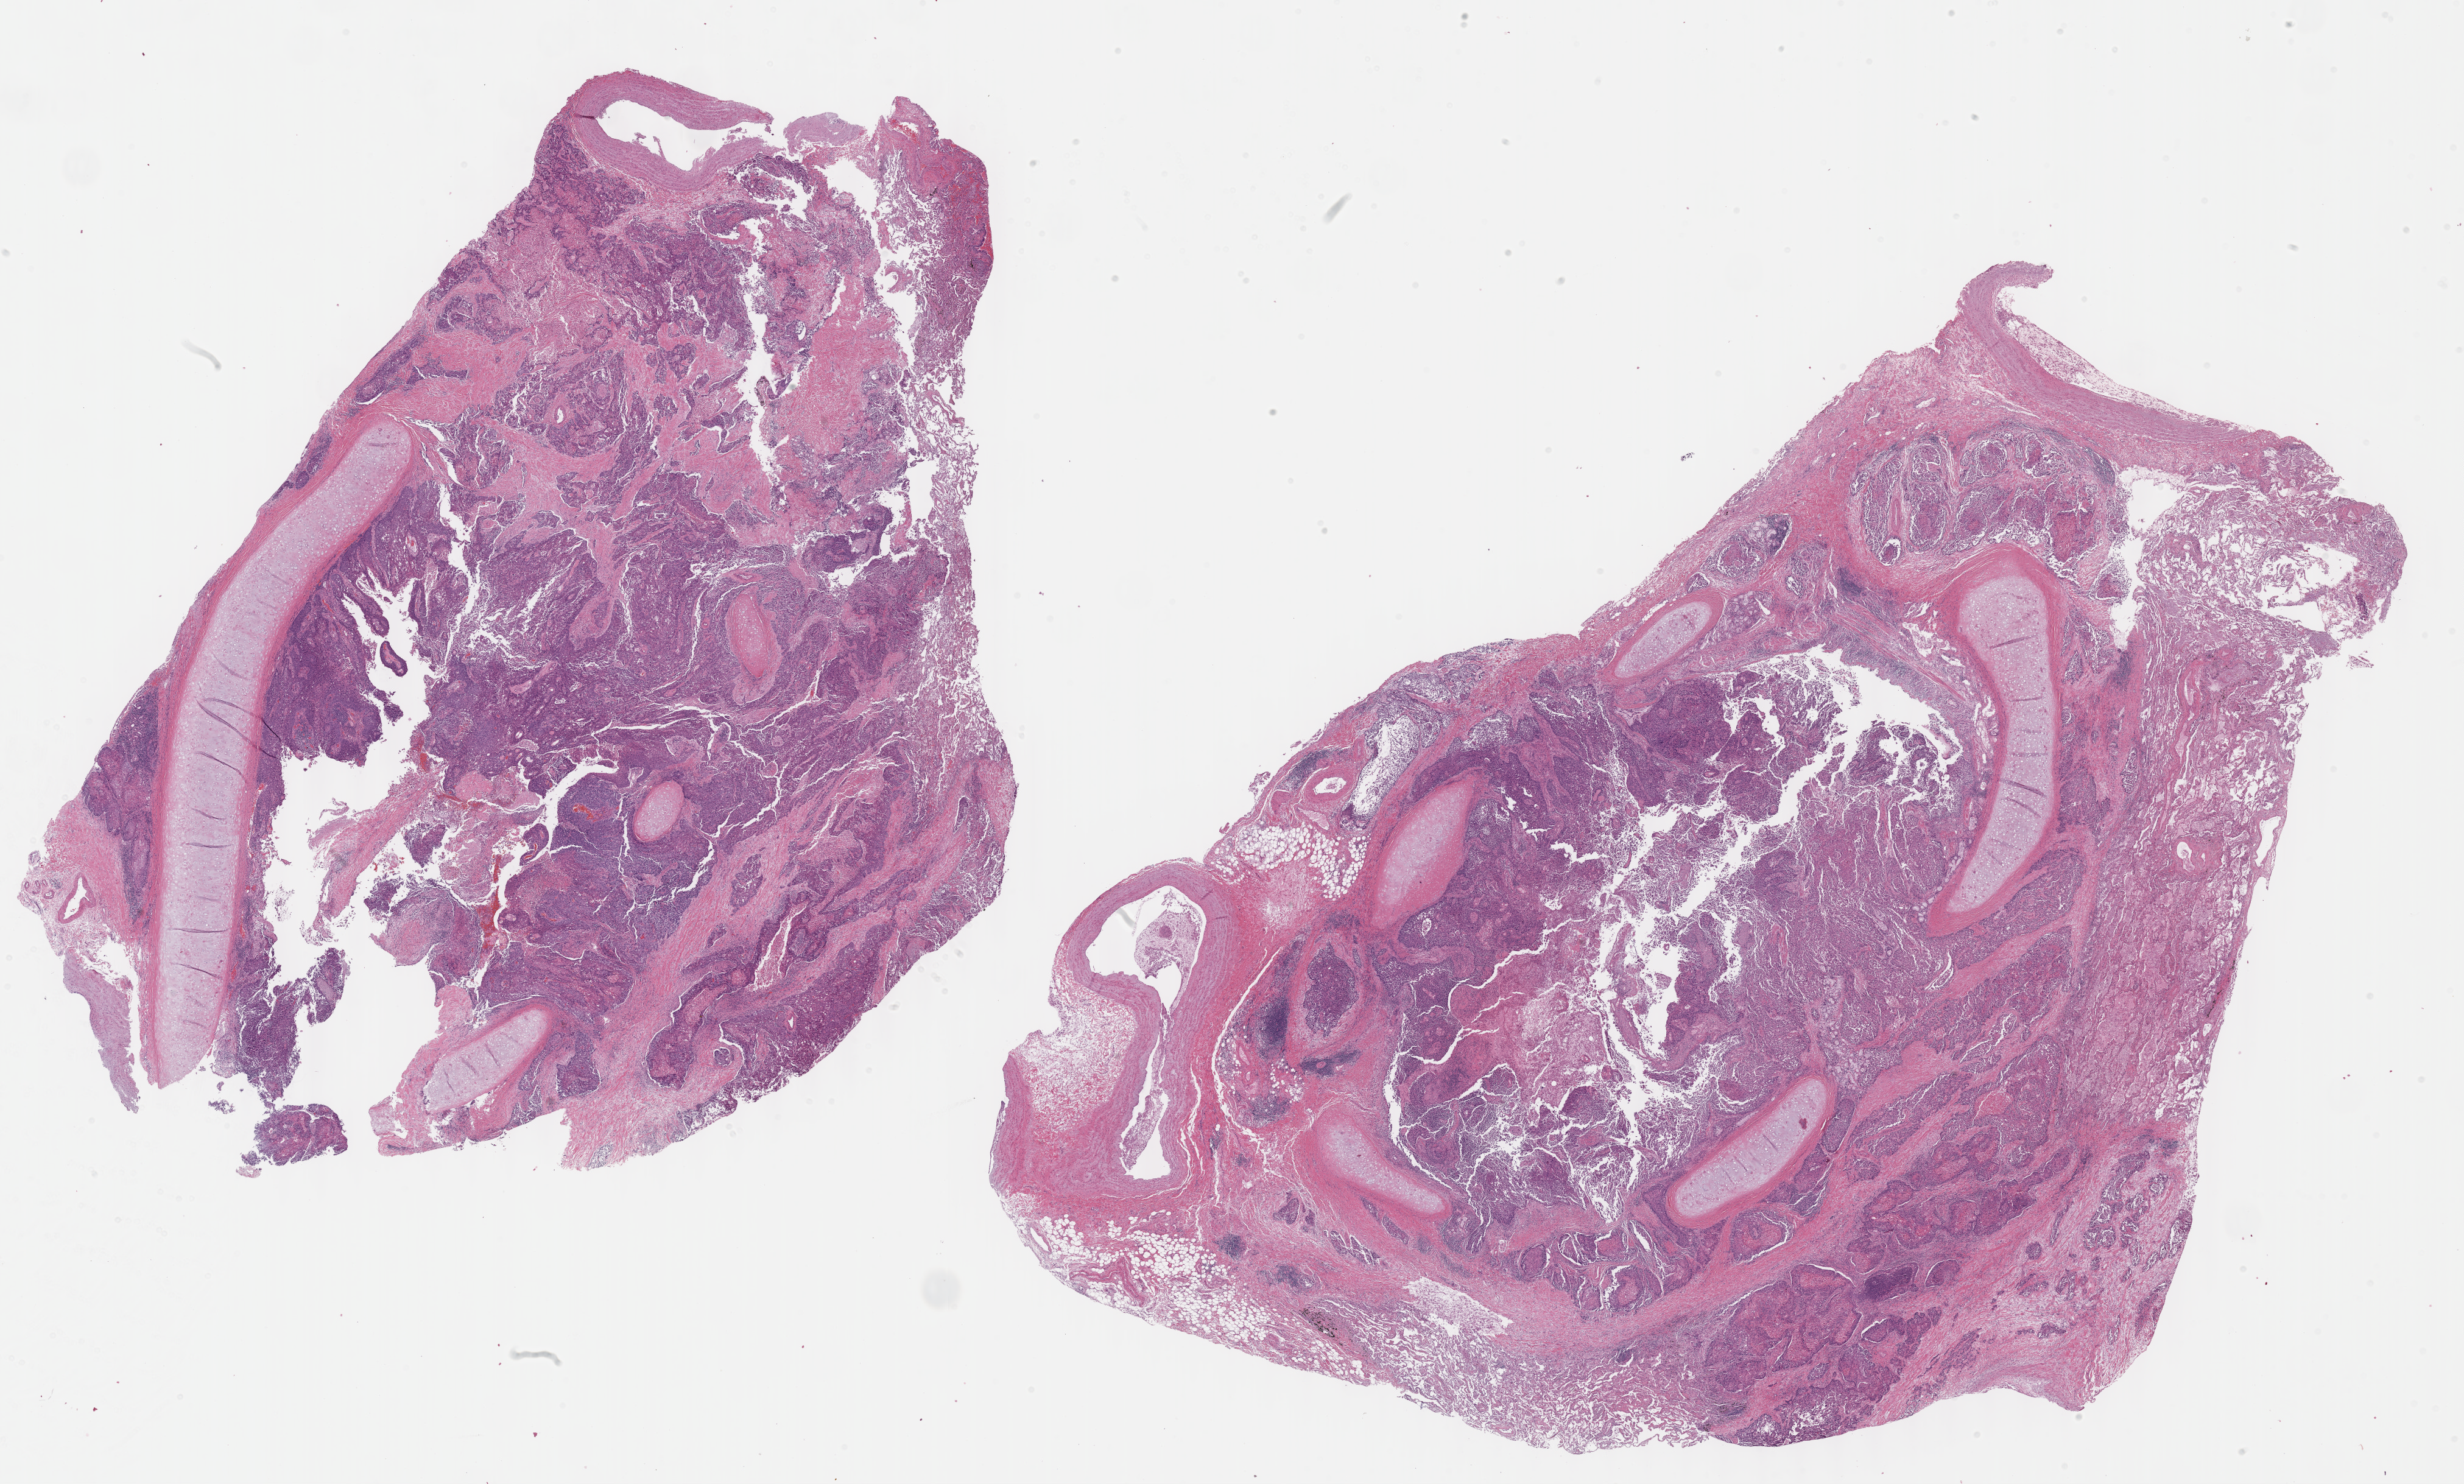
Whole-slide histology image, H&E-stained, shown as a low-resolution overview of the whole scanned area (about 32.7 x 19.7 mm, from a 40x scan), formalin-fixed paraffin-embedded (FFPE) diagnostic section, primary tumour sample from the lung. Male, age 74 years at initial diagnosis.
Laterality: left. AJCC pathologic stage: IA. Diagnosis: Squamous cell carcinoma, NOS (lower lobe, lung).